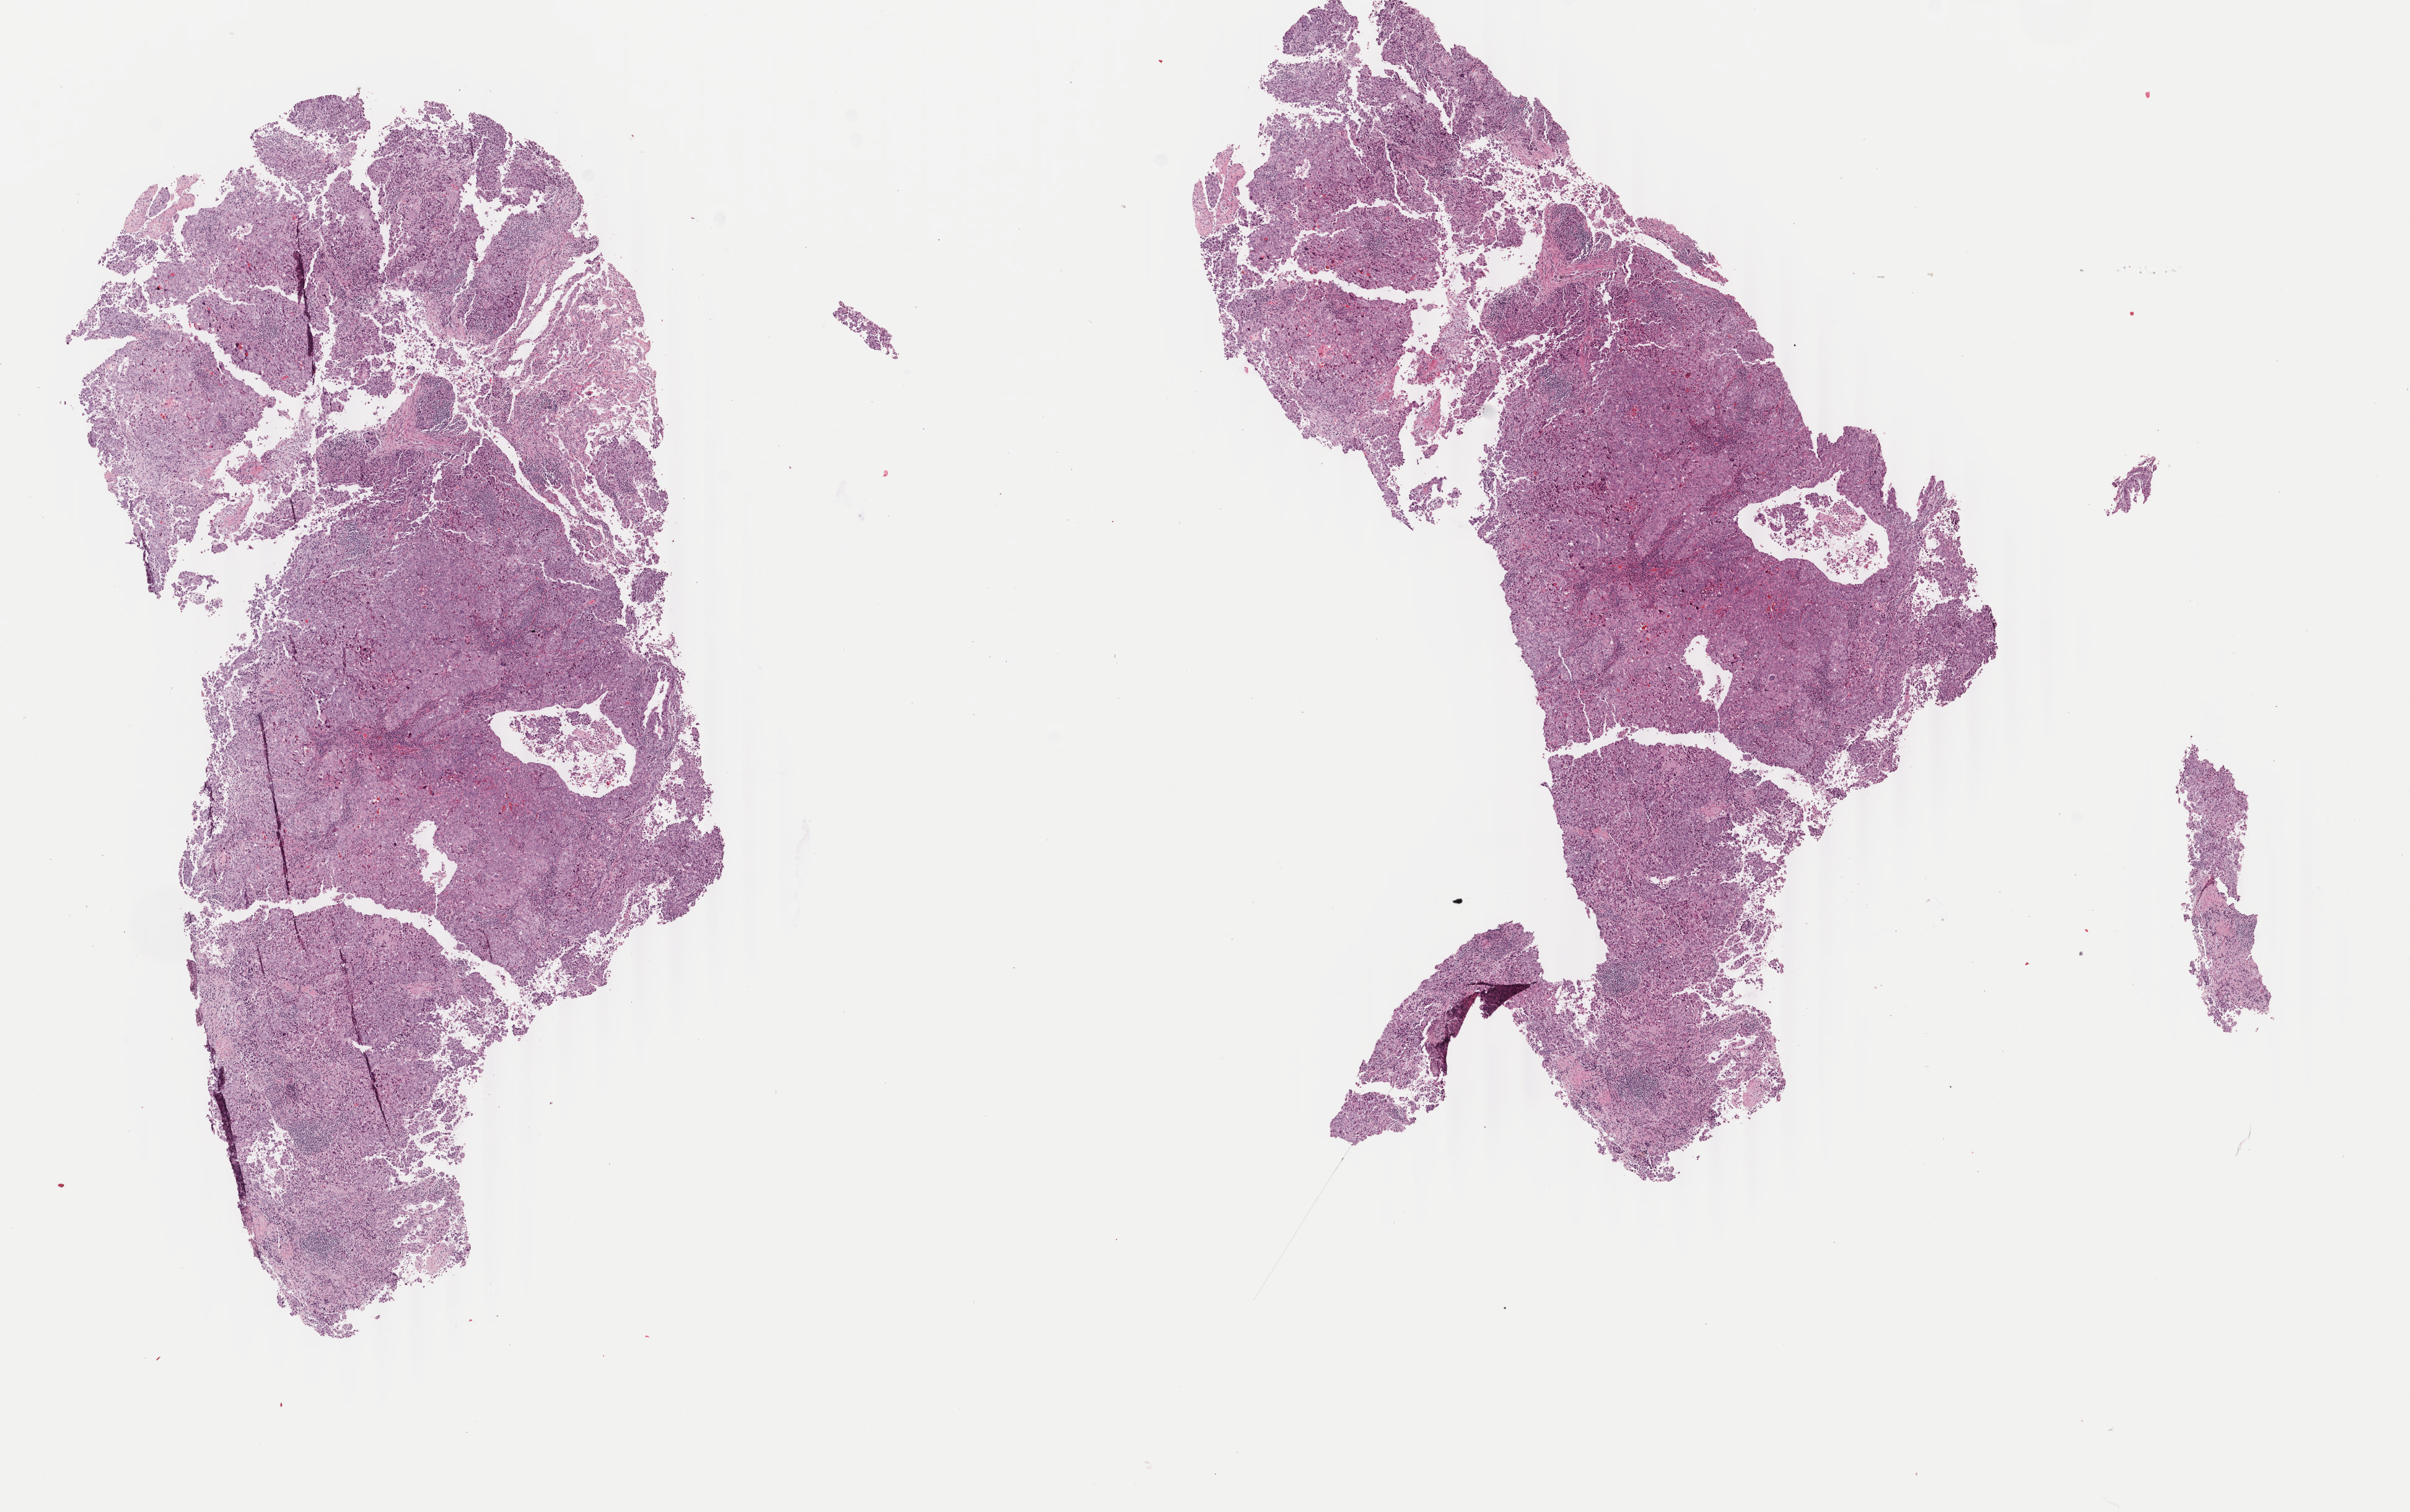
Digitized H&E-stained tissue section (whole slide), low-resolution overview of the scanned area, about 15.5 x 9.7 mm, frozen section, sample: primary tumour, lung. Female, age 33 years at initial diagnosis. Pathologist review of this section (percent, as recorded): tumour cells 75%, tumour nuclei 75%, normal cells 0%, stromal cells 21%, necrosis 4%. Inflammatory infiltration, as recorded: lymphocyte infiltration 4%, monocyte infiltration 2%, neutrophil infiltration 2%.
- AJCC pathologic stage: IB
- histologic diagnosis: Adenocarcinoma, NOS (upper lobe, lung)